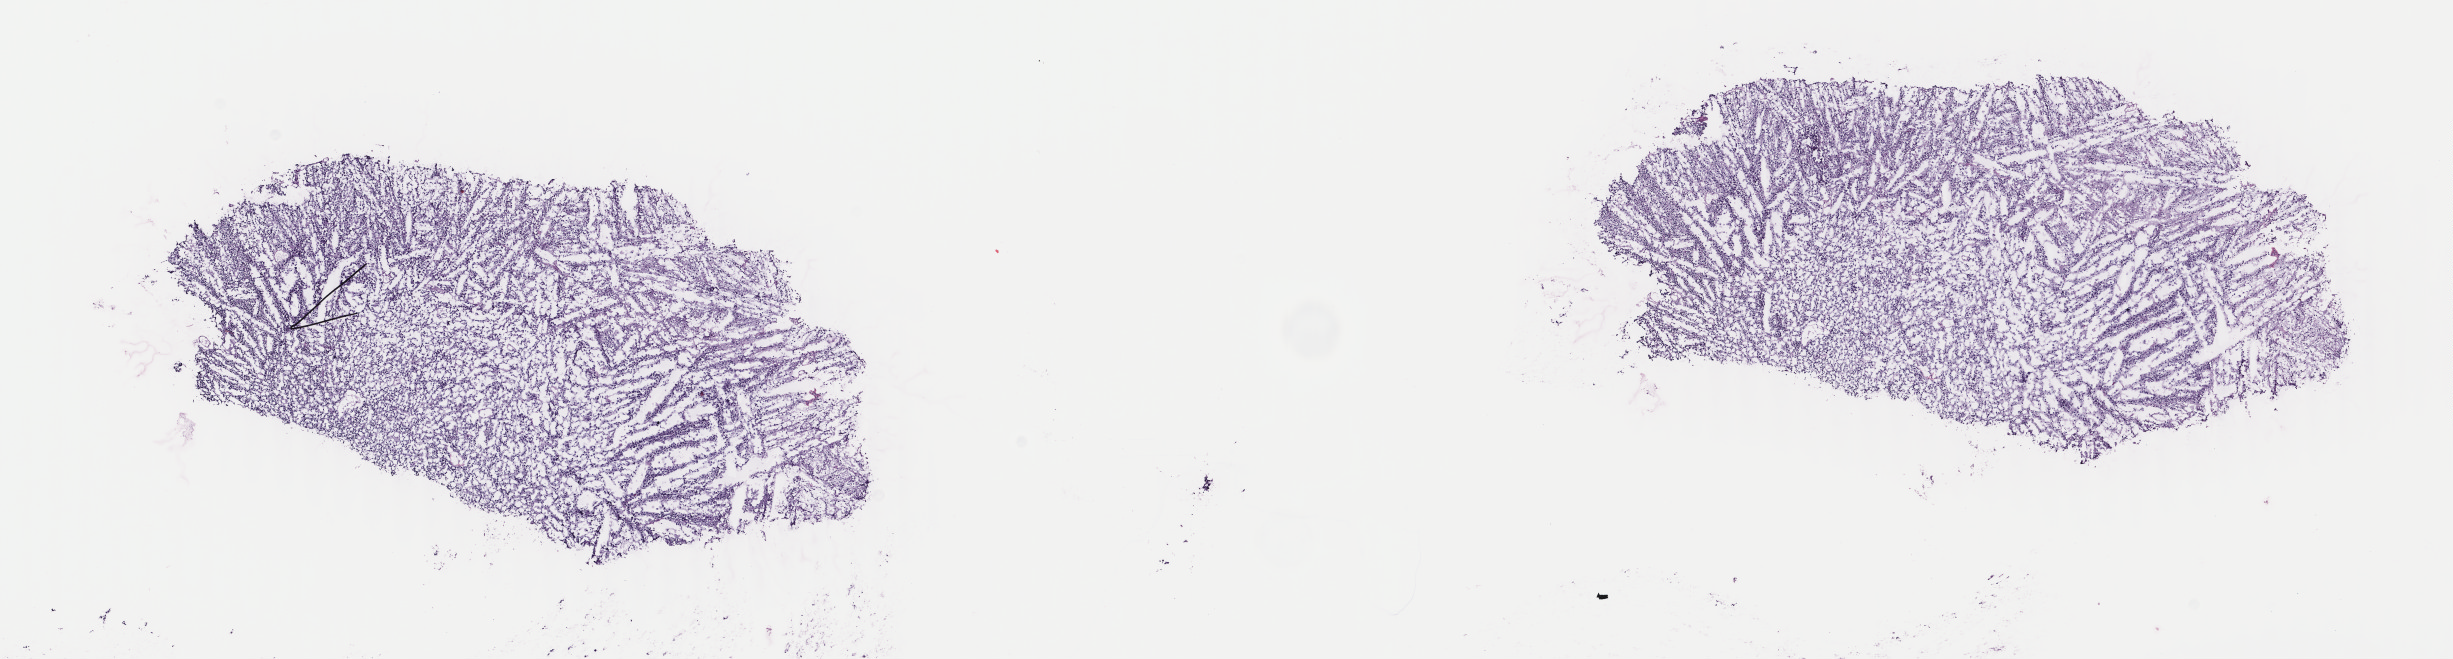
Digitized H&E-stained tissue section (whole slide), shown as a low-resolution overview of the whole scanned area (about 19.5 x 5.2 mm, slide scanned at 40x); frozen section; brain, primary tumour sample. Patient: female, age at initial diagnosis 73 years. Histologic grade: G2 (moderately differentiated). Composition of this section per pathologist review: tumour cells 80%, tumour nuclei 90%, normal cells 10%, stromal cells 10%, necrosis 0%. Inflammatory infiltration, as recorded: lymphocyte infiltration 0%, monocyte infiltration 0%, neutrophil infiltration 0%.
Histologic diagnosis: Mixed glioma (cerebrum).